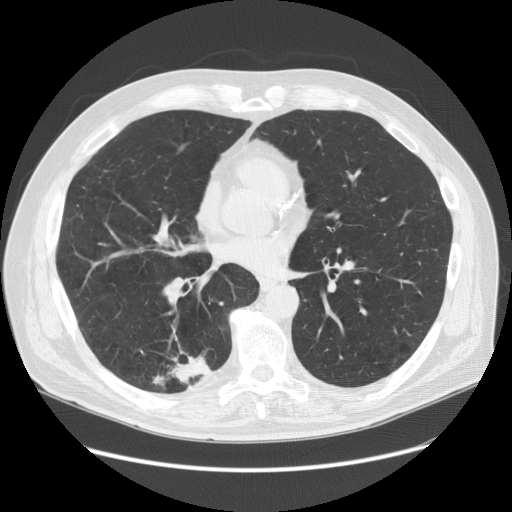
Axial slice from a low-dose chest CT screening exam; first (baseline) screen; lung window (W 1500 / L -600 HU); 2.5 mm slice thickness; slice 81 of 149 in the series. Male participant, aged 68 years at enrolment. Former smoker at enrolment.
- Expert-annotated lung lesion, box from (x=124, y=335) to (x=225, y=409) px.
- Reader record for this screening exam (exam-level; its link to the box is not recorded): non-calcified nodule or mass ≥4 mm, right lower lobe, 37 × 20 mm, spiculated (stellate) margins, soft tissue attenuation.
- Official screen result: positive, change unspecified: nodule(s) >= 4 mm or enlarging nodule(s), mass(es), or other non-specific abnormalities suspicious for lung cancer.
- Later outcome: lung cancer diagnosed 24 days after this screen — adenosquamous carcinoma, right lower lobe, poorly differentiated (G3), stage IIIA (AJCC 6th edition), 30 mm at pathology.